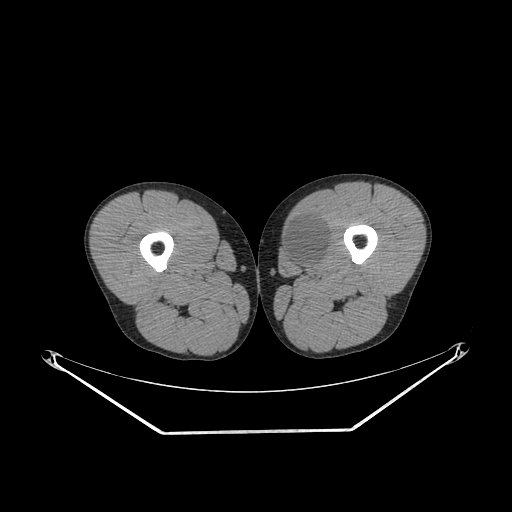
CT of an extremity soft-tissue mass (from a PET/CT study), one axial slice; position 251 of 311 along the scan axis; reconstruction kernel SOFT; soft-tissue window (W 400 / L 40 HU); 3.75 mm slice thickness; 512 × 512 image matrix, field of view 500 × 500 mm. Male patient. Case-level facts recorded for this patient, not image findings: histological type: mixoid liposarcoma; grade: low; site of the primary tumour: left thigh.
Annotated regions visible in this slice (expert contour drawn on MRI and transferred to this co-registered scan by the dataset authors):
- gross tumour volume (mass): box from (x=283, y=217) to (x=330, y=270) px